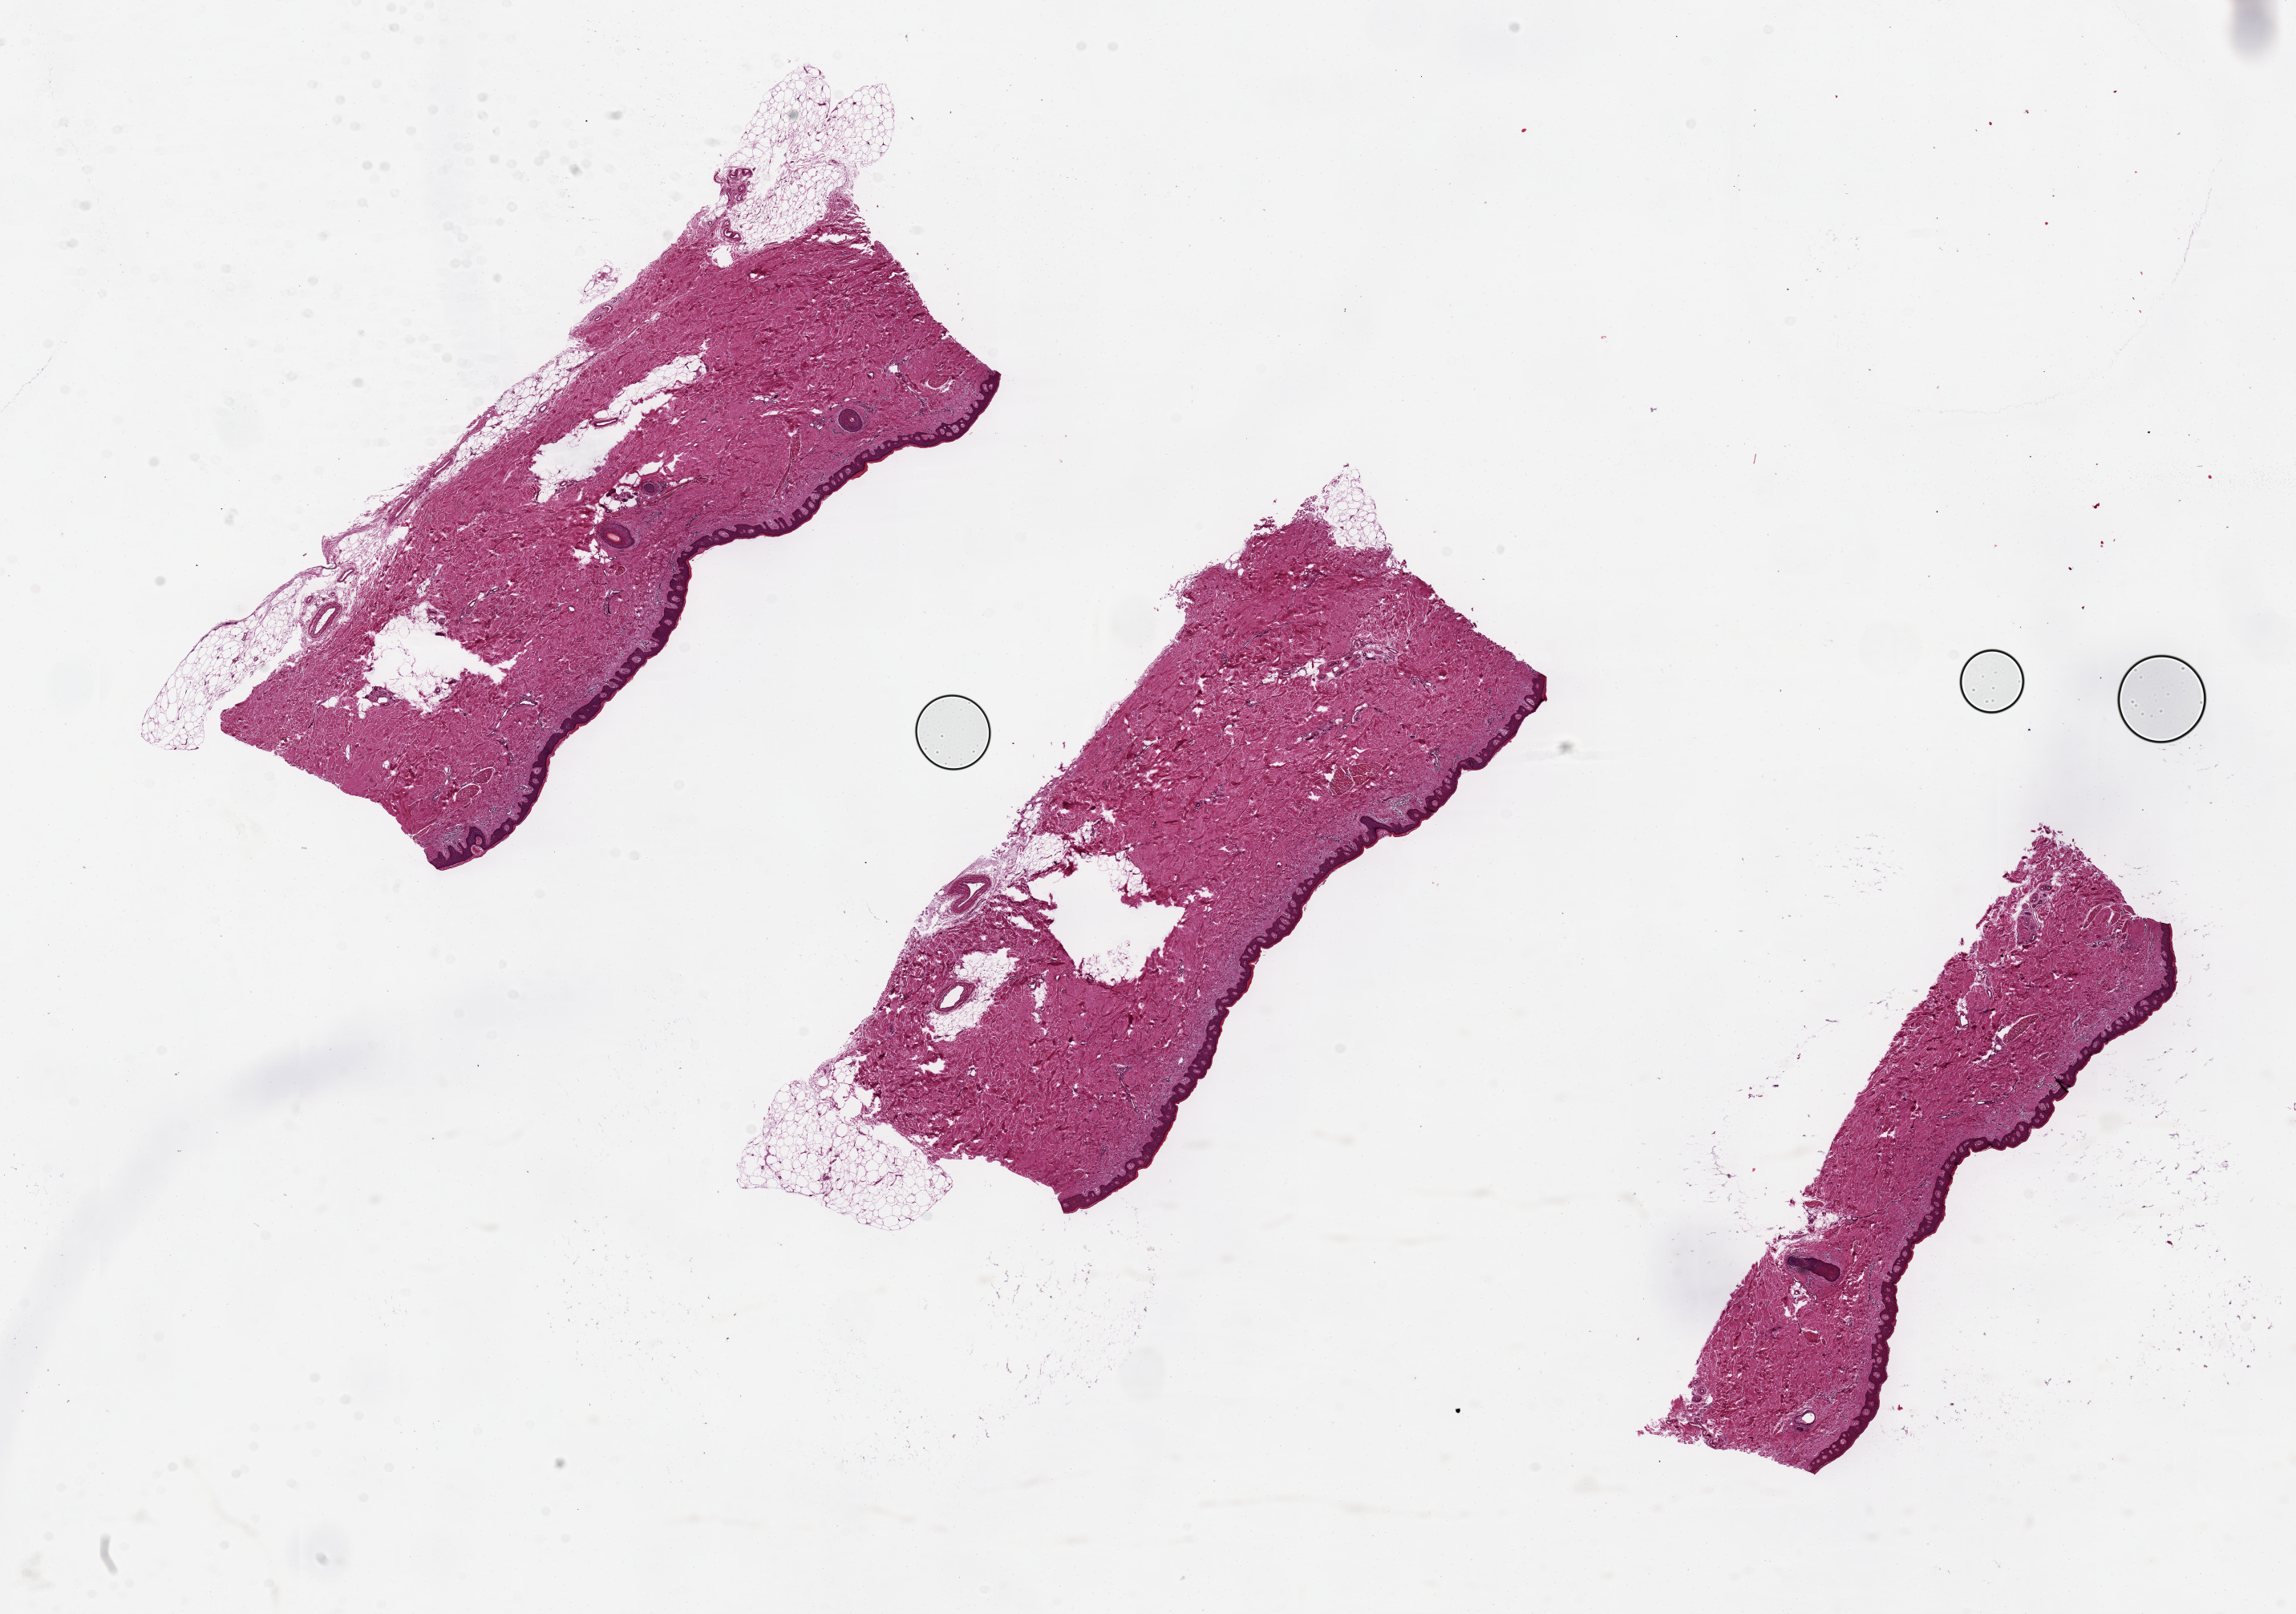
Whole-slide image, hematoxylin and eosin (H&E) stain, a low-resolution overview of the entire scanned area, about 22.6 x 15.9 mm. PAXgene-fixed paraffin-embedded (PFPE) section. Section of skin of lower leg (target tissue). Donor tissue sample. Donor sex: male.
* review note (as recorded): Hollow defects in dermal fat